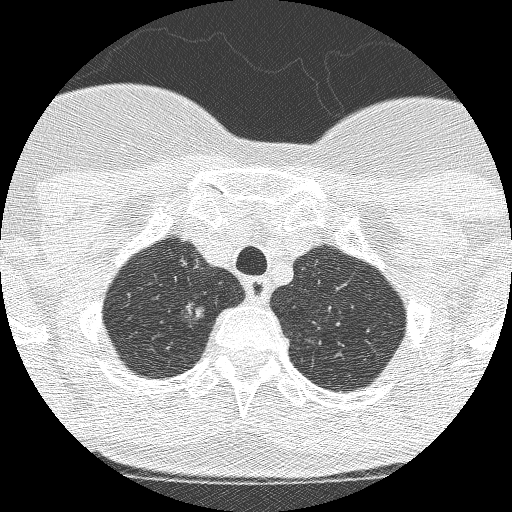
Chest CT (low-dose screening protocol), one axial image. Second annual screen. Lung window (W 1500 / L -600 HU). 1.25 mm slice thickness. Lung (sharp) reconstruction kernel (BONE). Slice 212 of 250 in the series. Female participant, aged 61 years at enrolment. Current smoker at enrolment.
• Expert reader's lesion annotation, box from (x=170, y=296) to (x=215, y=333) px.
• The exam's reader record, not a measurement of the box and not confirmed to be the same lesion: non-calcified nodule or mass ≥4 mm, right upper lobe, 11 × 8 mm, poorly defined margins, mixed attenuation, pre-existing on the prior screen: yes; interval growth: yes.
• Later outcome: lung cancer diagnosed 28 days after this screen — adenocarcinoma, NOS, right upper lobe, poorly differentiated (G3), 12 mm at pathology.